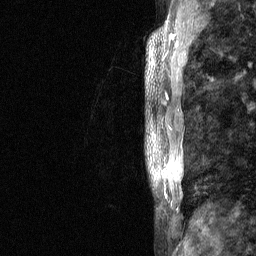
Breast MRI (dynamic contrast-enhanced), one sagittal slice; slice 15 of 64 in the series (ordered by position); dynamic contrast-enhanced study with each time point stored as its own series, time point 2 of 3 at this slice position (early post-contrast, ordered by acquisition time); 1.5 T; TE 4.8 ms, TR 27 ms; 2 mm slice thickness; 256 × 256 image matrix, field of view 180 × 180 mm. Patient: female, 36 years. From the clinical record (not read from this slice): setting: breast cancer imaged before/during neoadjuvant chemotherapy; receptor status: HR-positive, HER2-negative.
Annotated regions visible in this slice (semi-automatic segmentation, software-assisted and operator-edited):
- analysis volume of interest (the breast-tissue region the enhancement analysis was run in; not a lesion): bounding box (x1, y1, x2, y2) in pixels: (145, 12, 212, 238)
- tumour enhancement mask (voxels above the 90 % enhancement threshold inside the analysis volume of interest): (169, 34, 178, 46)